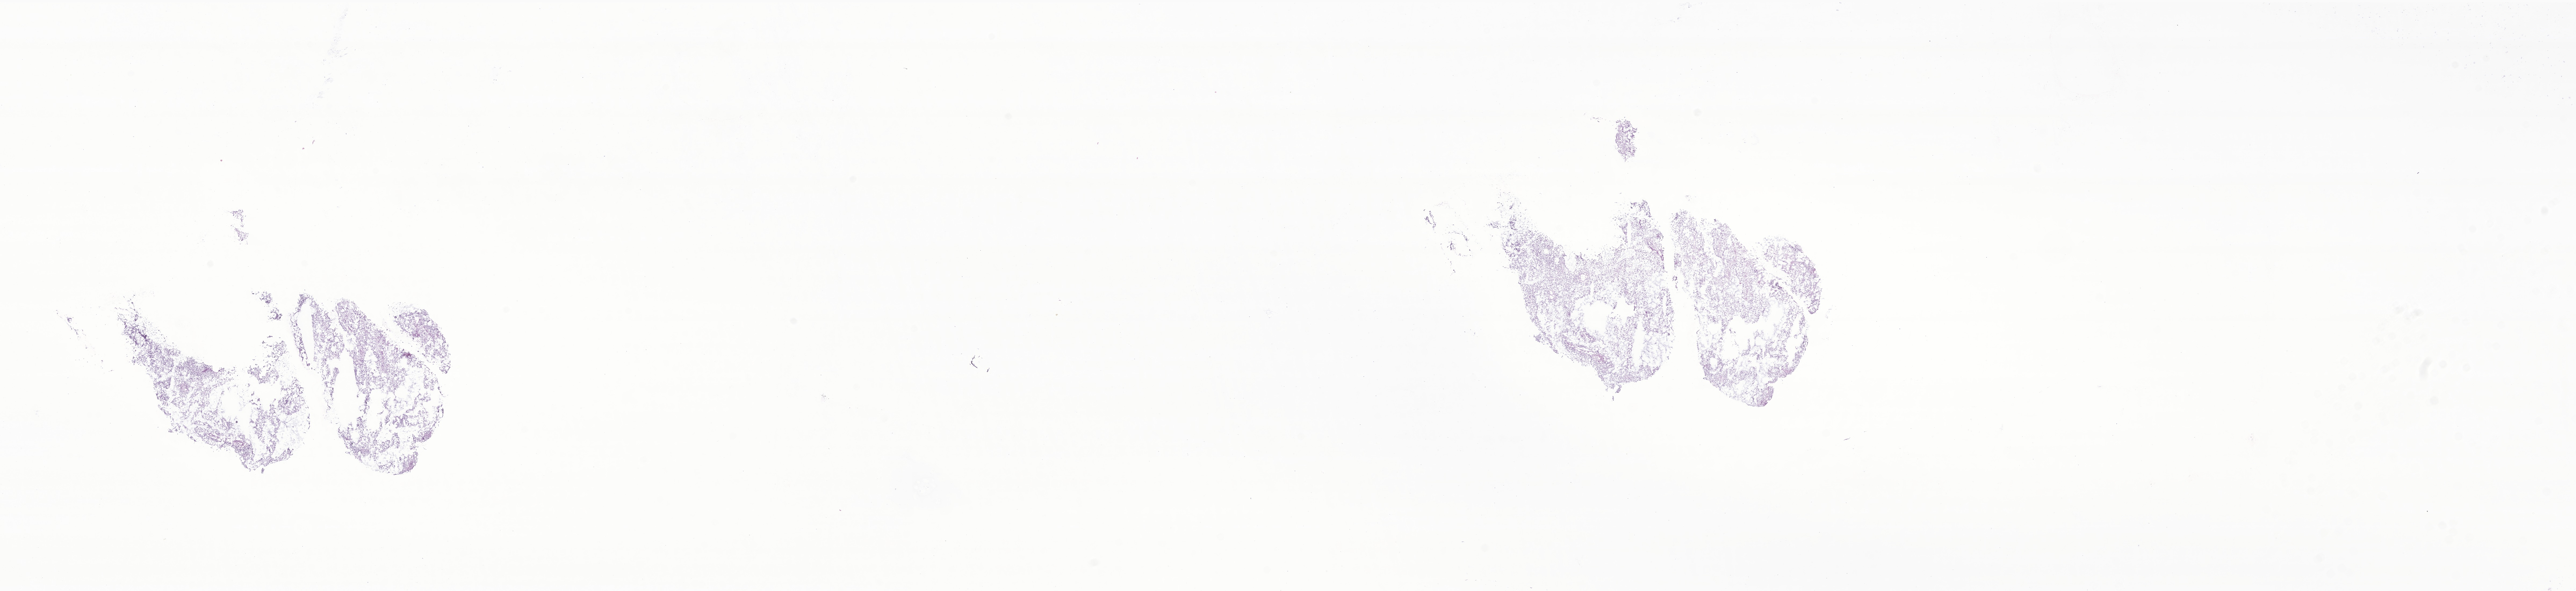
Whole-slide image, hematoxylin and eosin (H&E) stain of tumor tissue from the brain, whole scanned area (about 40.4 x 9.3 mm) shown as a low-resolution overview, frozen section (OCT-embedded). Female patient, age 186 months (15 years 6 months).
Diagnosis: Pilocytic astrocytoma.